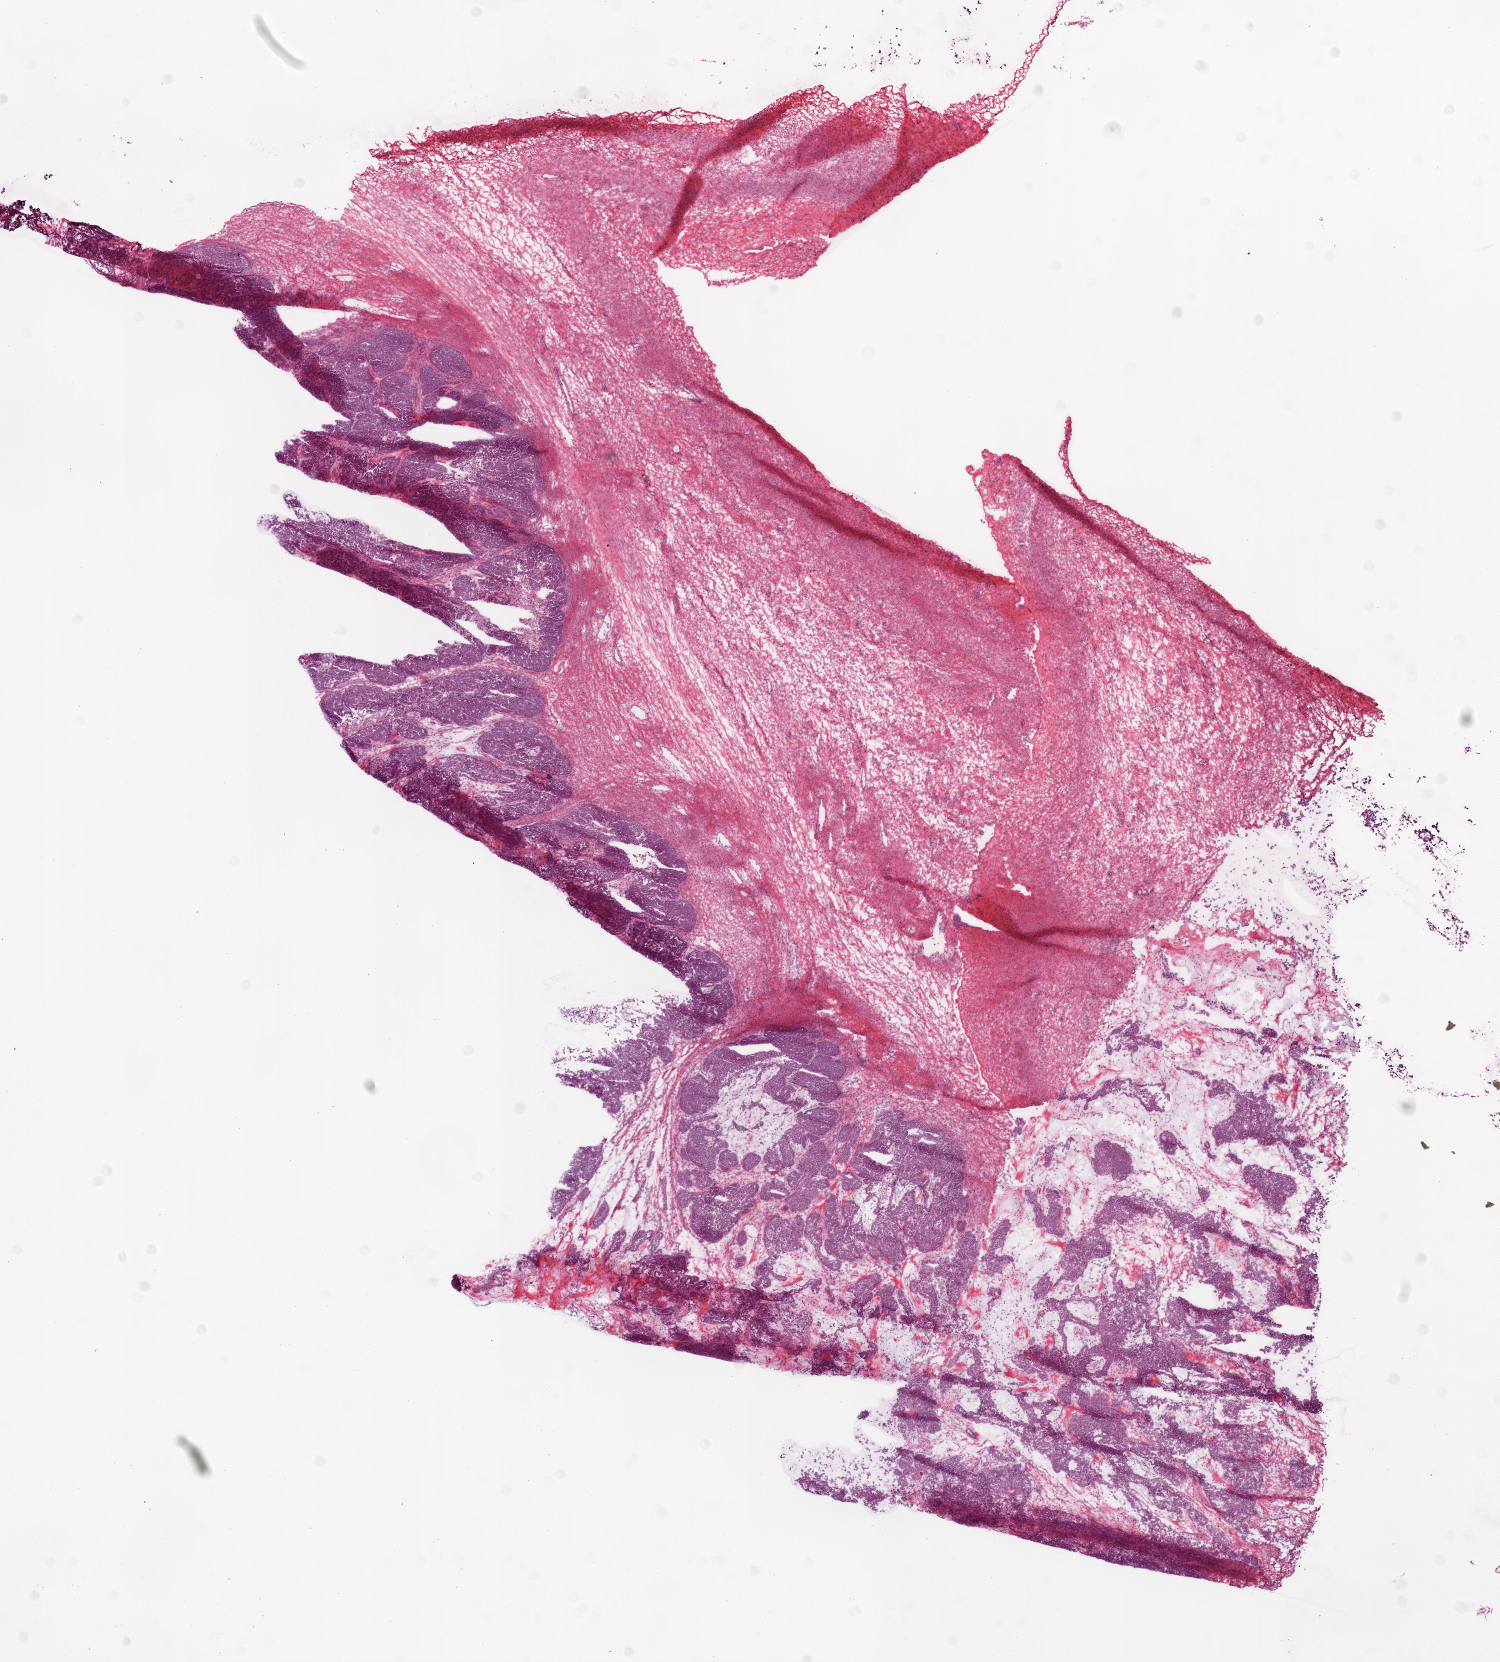
Whole-slide histology image, H&E-stained, a low-resolution overview of the entire scanned area, about 12.0 x 13.3 mm (slide scanned at 20x). Frozen section from the bottom of the tissue portion. Primary tumour sample from the ovary. Female, age 40 years at initial diagnosis. Histologic grade: G2 (moderately differentiated). Slide review estimates, as recorded: tumour cells 69%, tumour nuclei 70%, normal cells 0%, stromal cells 30%, necrosis 1%.
Diagnosis: Serous cystadenocarcinoma, NOS. Laterality: bilateral. FIGO stage: IIC.